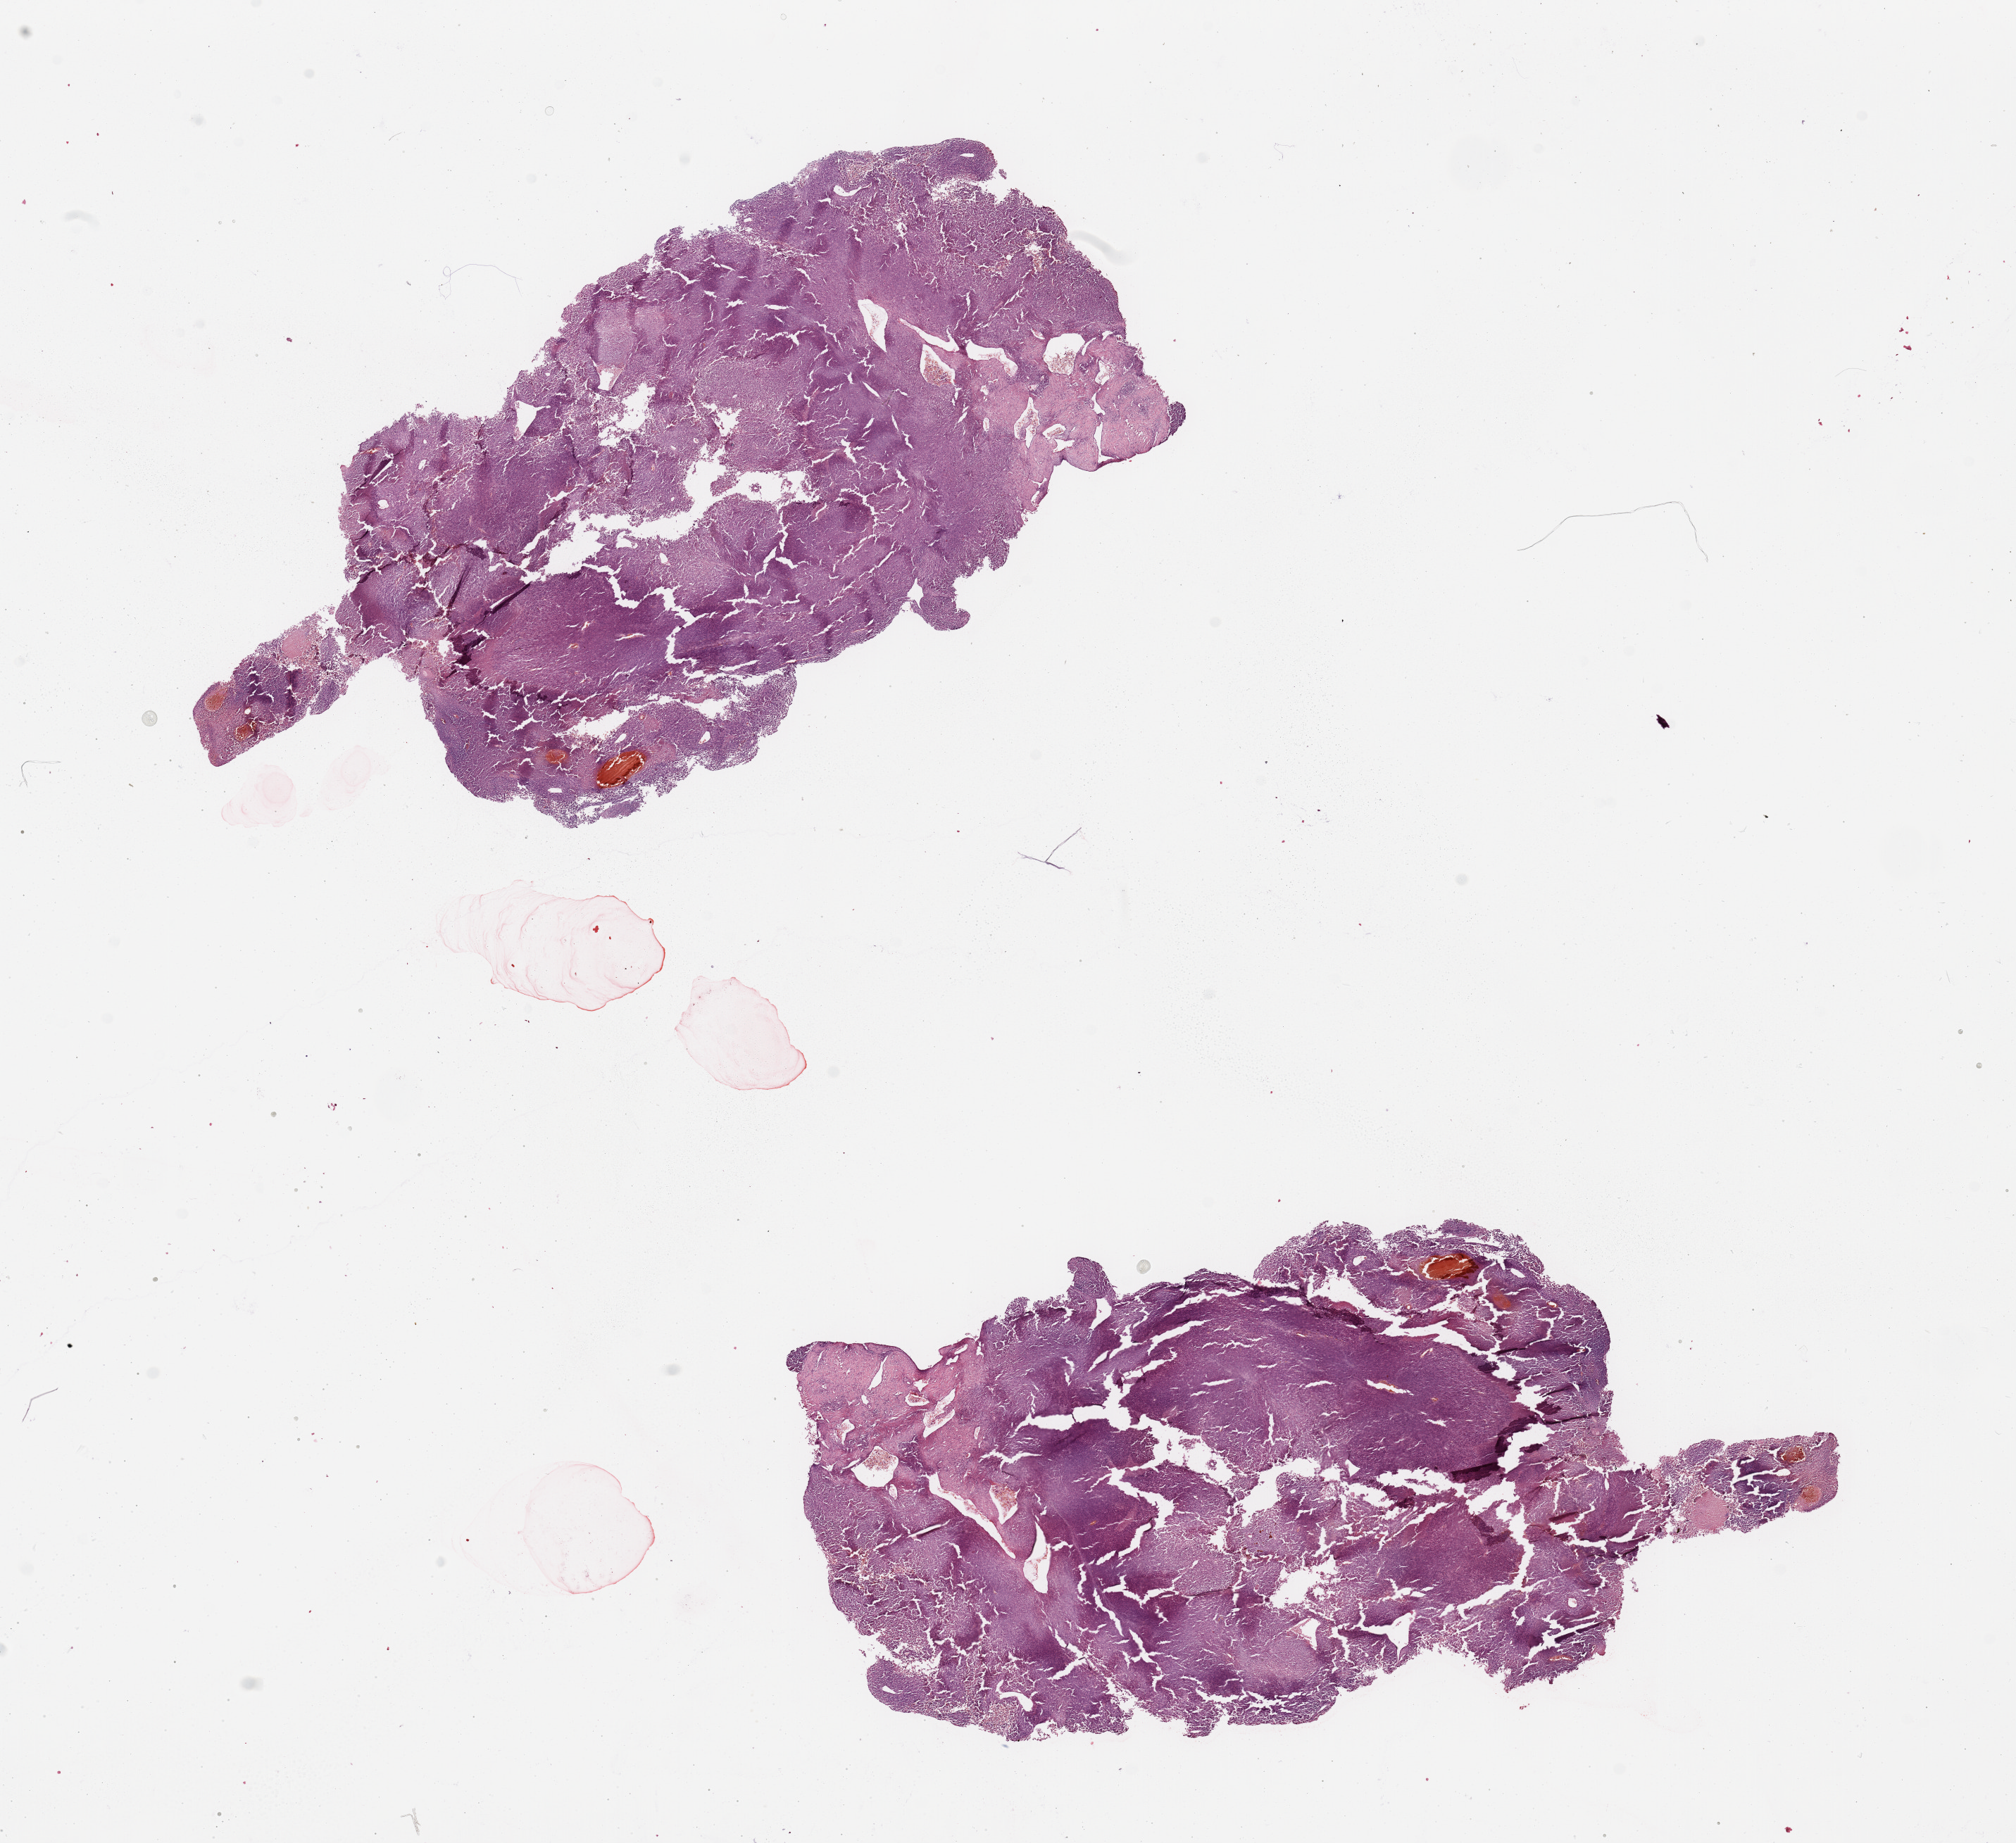
Whole-slide histology image, Hematoxylin and eosin (H&E) stained, low-resolution overview of the scanned area, about 22.6 x 20.7 mm, melanoma tumour tissue; sampled site not recorded. Patient: male, age 75 years.
- histologic diagnosis: Malignant melanoma, NOS
- AJCC pathologic stage: IIC
- primary tumour site (as recorded): trunk